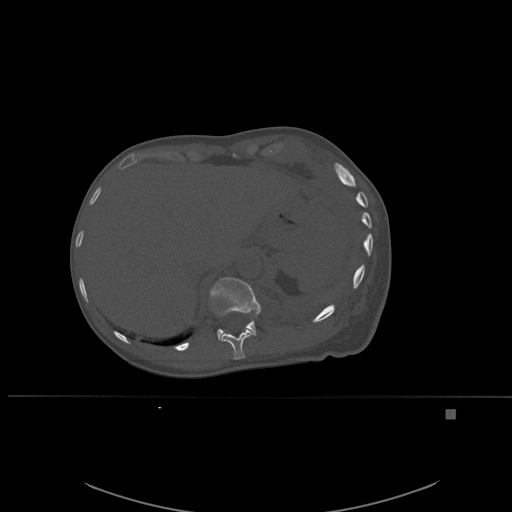
CT including the spine, one axial slice; position 291 of 537 along the scan axis; bone window (W 1800 / L 400 HU); 1.5 mm slice thickness; 512 × 512 image matrix, field of view 440 × 440 mm. Patient: female, 45 years. Case-level facts recorded for this patient, not image findings: primary cancer: lung.
Structures marked on this image (semi-automatic segmentation, software-assisted and operator-edited):
- T11 vertebra: bounding box <210,298,254,360> (left, top, right, bottom; pixels)
- T12 vertebra: <209,277,261,340>